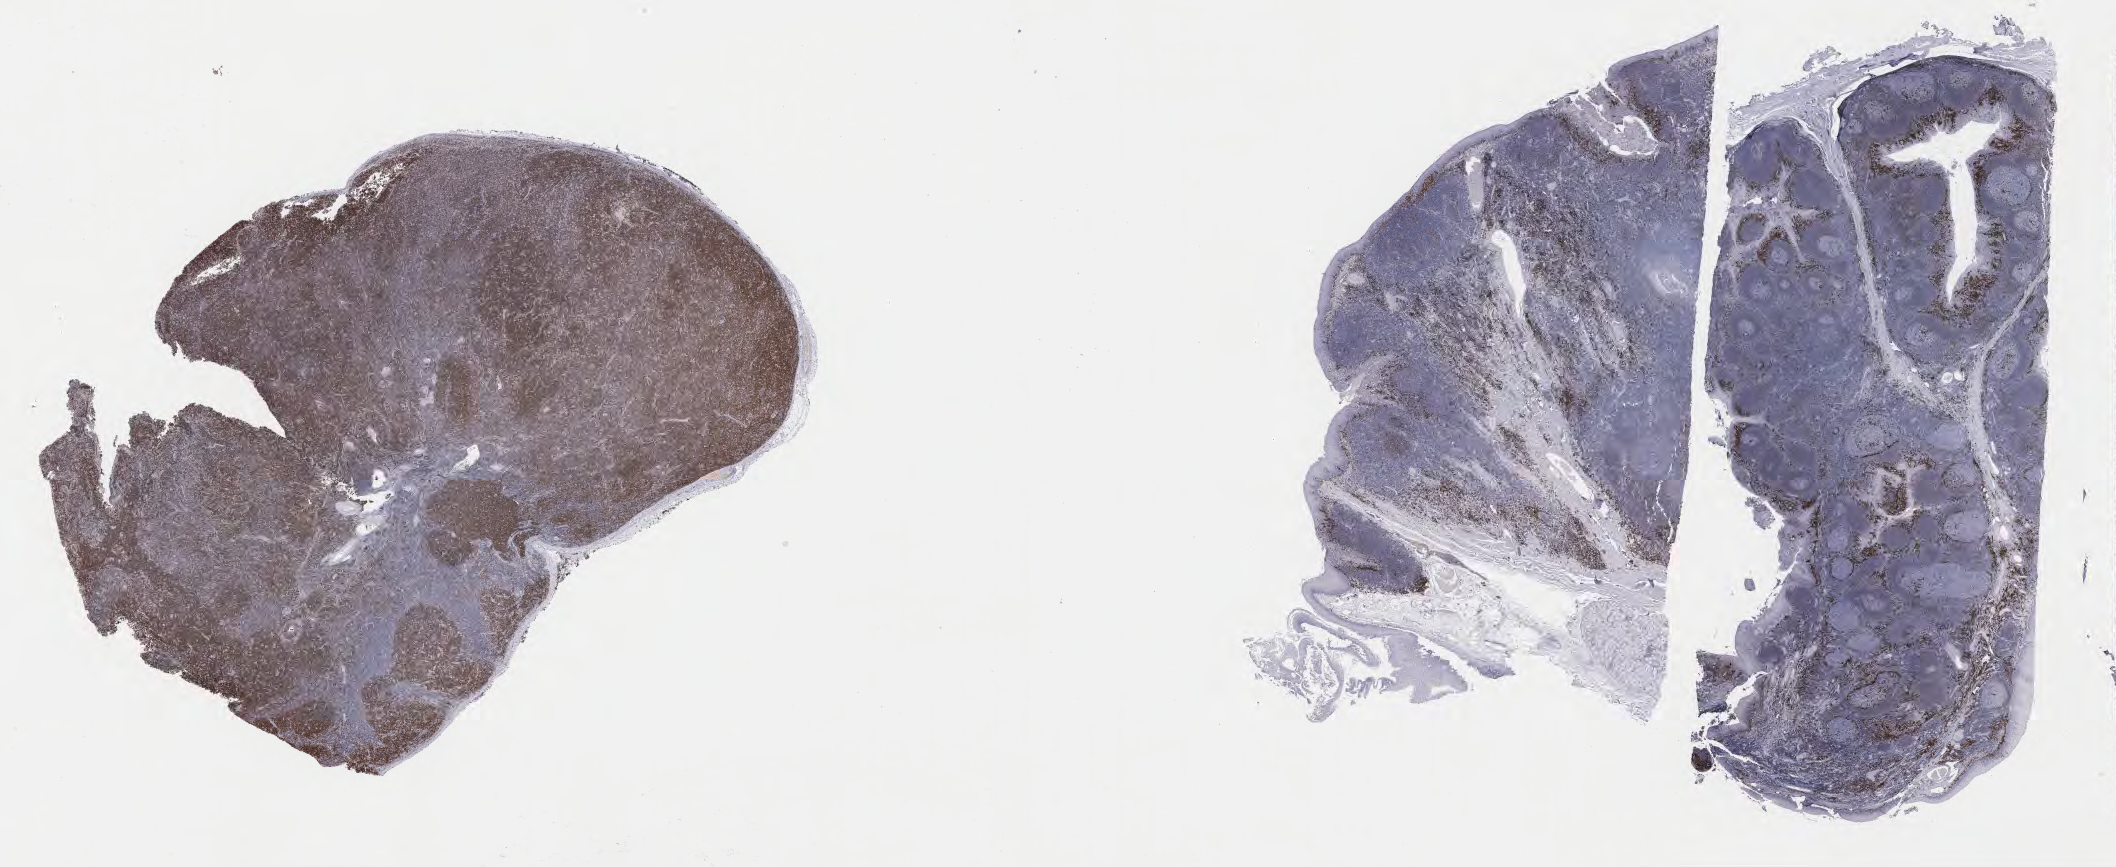
Immunohistochemistry (IHC) whole-slide image stained for IRF4/MUM1, a low-resolution overview of the entire scanned area, about 34.2 x 14.0 mm; tumor tissue; anatomic site: lymph node. Patient: male, 32 years old.
Histologic diagnosis: Diffuse large B-cell lymphoma, NOS.